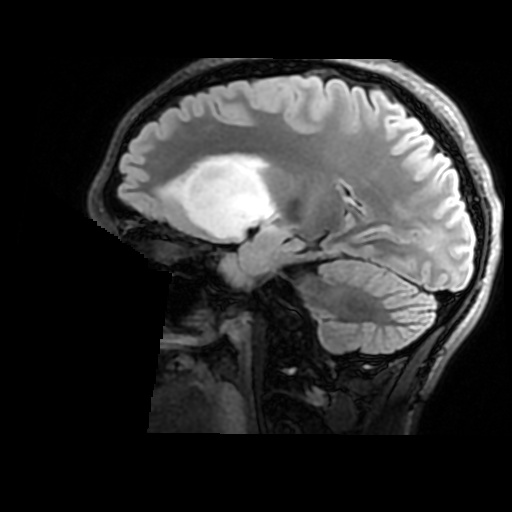
Brain MRI from a brain-tumour surgery series, one sagittal slice; slice 106 of 176 in the series (ordered by position); T2 FLAIR; 512 × 512 image matrix, field of view 240 × 240 mm. From the clinical record (not read from this slice): histopathology: Astrocytoma; WHO grade: 2; IDH mutation: yes; tumour location: Right Insular.
Structures marked on this image (expert manual segmentation):
- tumour: bounding box (x1, y1, x2, y2) in pixels: (170, 154, 279, 239)